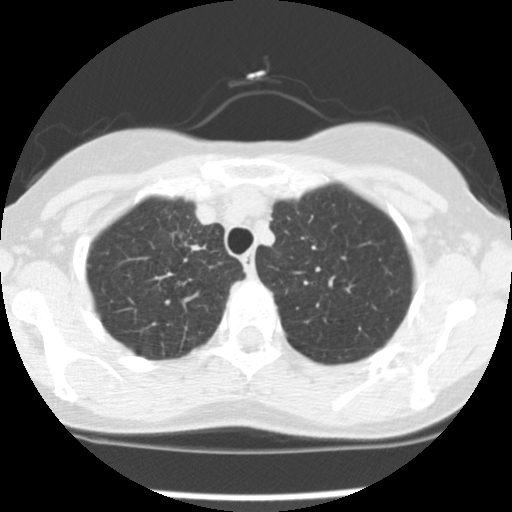
Low-dose screening chest CT, one axial slice. Position 125 of 157 along the scan axis. Reconstruction kernel STANDARD. Lung window (W 1500 / L -600 HU). 2.5 mm slice thickness. 512 × 512 image matrix.
Structures marked on this image (expert manual segmentation):
- lesion 1 (tumor, upper lobe of right lung): bounding box [x1, y1, x2, y2] px = [190, 244, 206, 251]